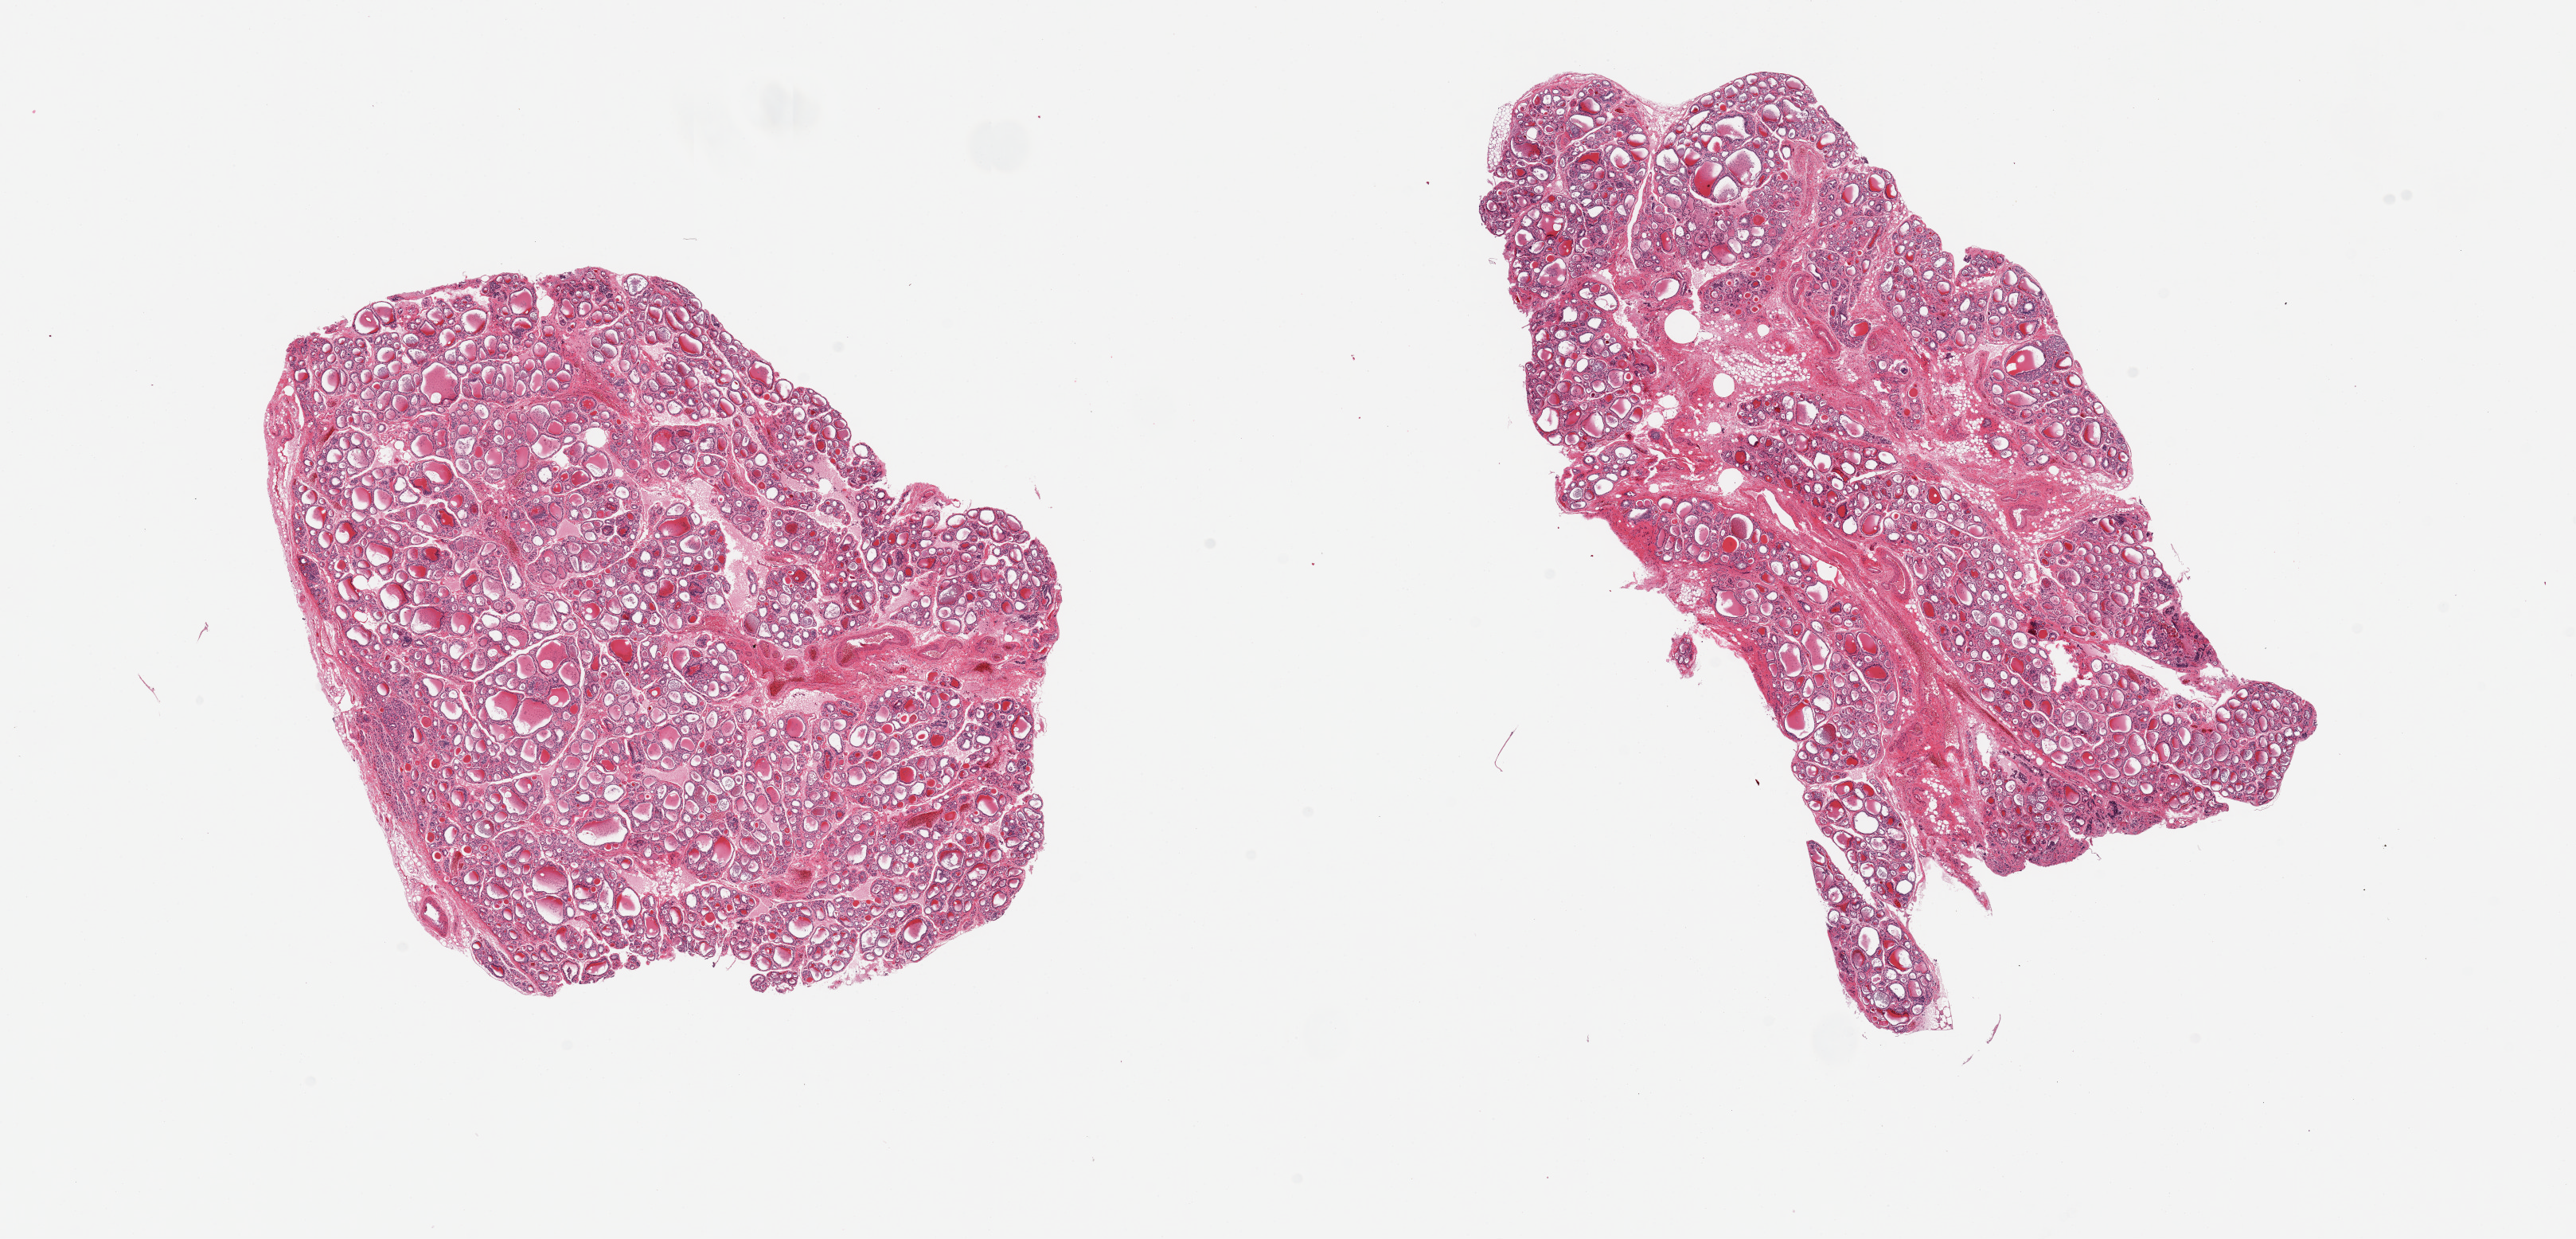
Digitized hematoxylin and eosin (H&E)-stained section — shown as a low-resolution overview of the whole scanned area (about 25.6 x 12.3 mm, from a 20x scan). PAXgene-fixed paraffin-embedded (PFPE) section. Target tissue: thyroid. Donor tissue sample. Donor: male.
Reviewer comment on this tissue sample: 2 pieces; 5% and 20% interspersed fat and vessels, some nodularity.